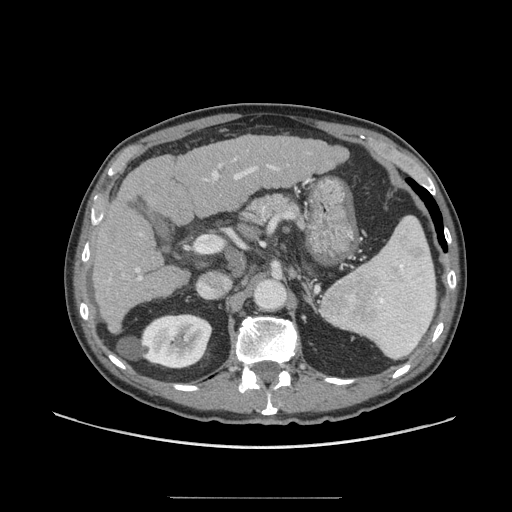
Contrast-enhanced abdominal CT (liver protocol), one axial slice; slice 37 of 71 in the series (ordered by position); 140 kVp; soft-tissue window (W 400 / L 40 HU); 2.5 mm slice thickness; 512 × 512 image matrix, field of view 400 × 400 mm. Case-level facts recorded for this patient, not image findings: diagnosis: hepatocellular carcinoma (patient treated with transarterial chemoembolisation; whether this scan precedes or follows treatment is not stated here); TNM stage (as recorded): Stage-I; Child-Pugh class: A; tumour differentiation: well differentiated; tumour nodularity: uninodular.
Annotated regions visible in this slice (semi-automatically segmented with operator editing):
- liver parenchyma outside the tumour (the mass and vessels are separate outlines, so this box may not span the whole liver): bounding box [x1, y1, x2, y2] px = [92, 134, 346, 332]
- liver vessels: [108, 159, 279, 282]